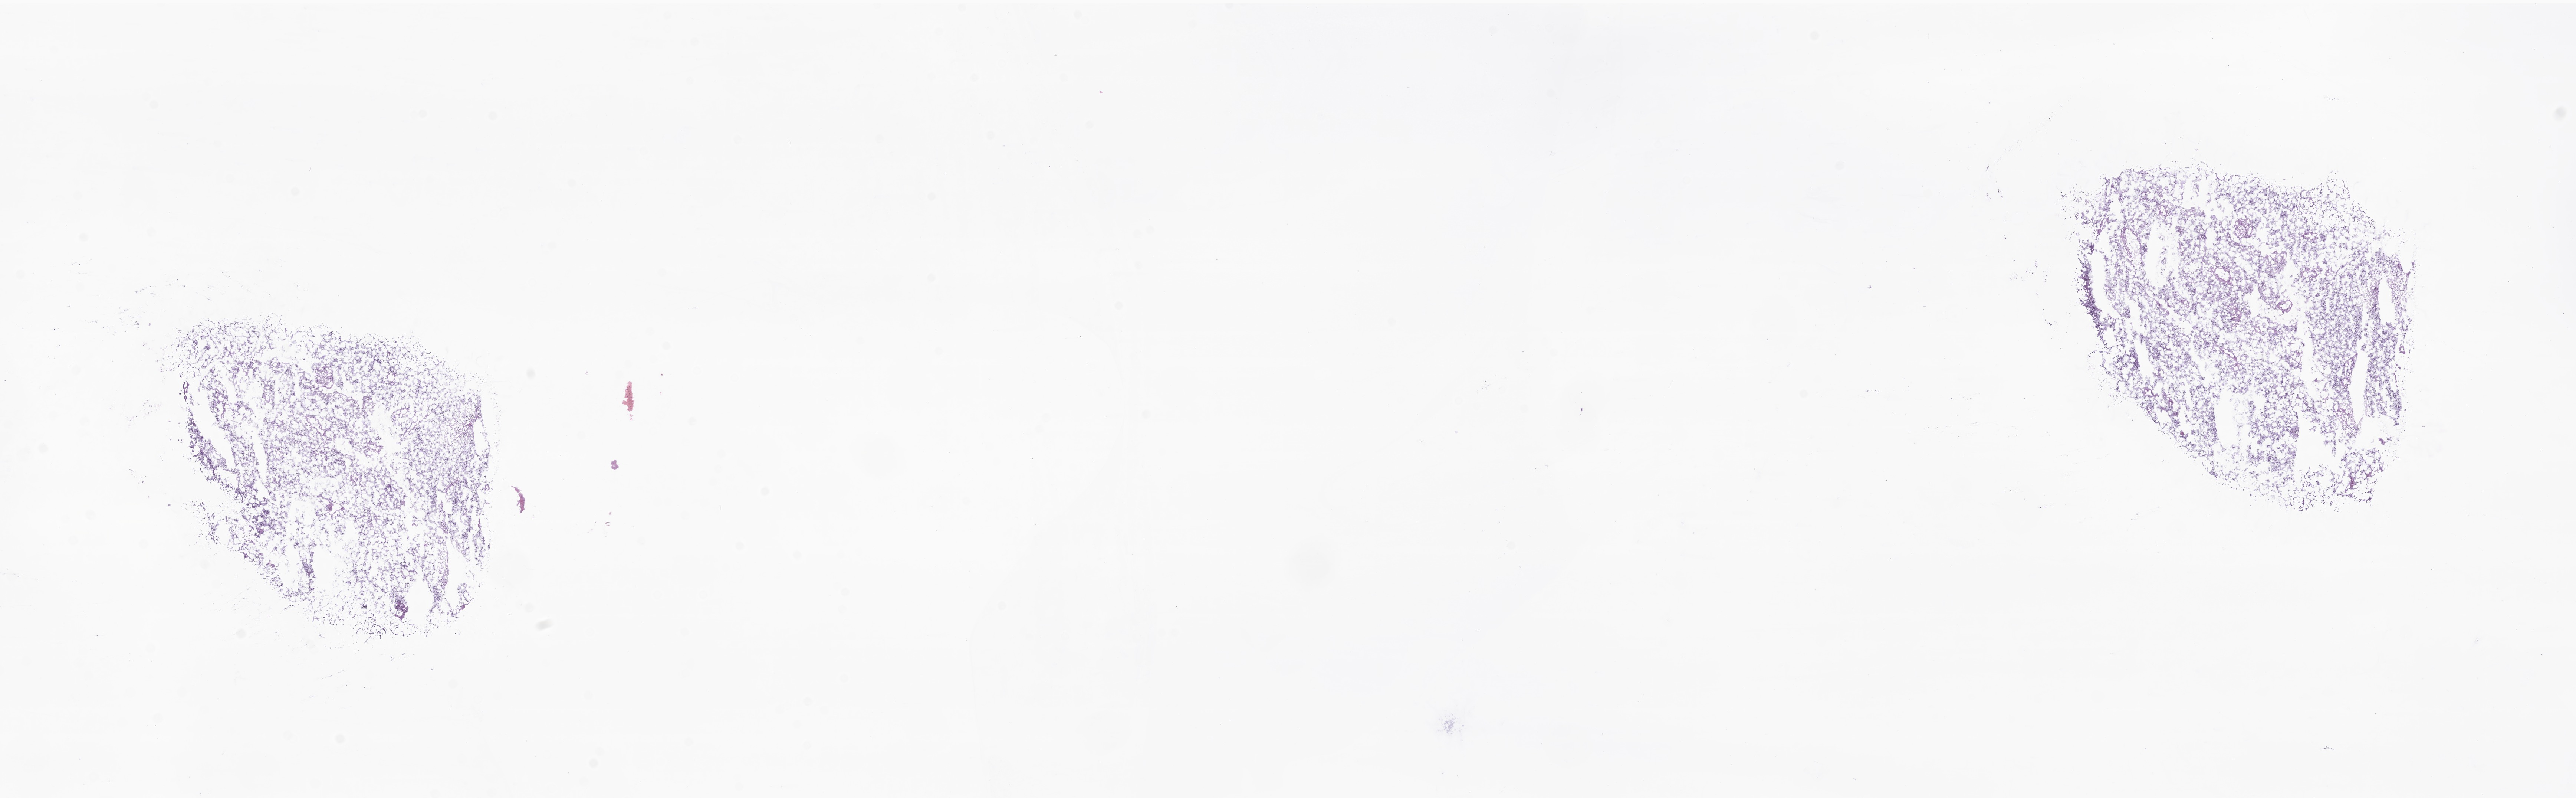
Whole-slide image, H&E stain of tumor tissue from the brain, a low-resolution overview of the entire scanned area, about 29.3 x 9.1 mm; frozen section (OCT-embedded). Patient: female, age 199 months (16 years 7 months).
- recorded diagnosis: Glioblastoma, NOS